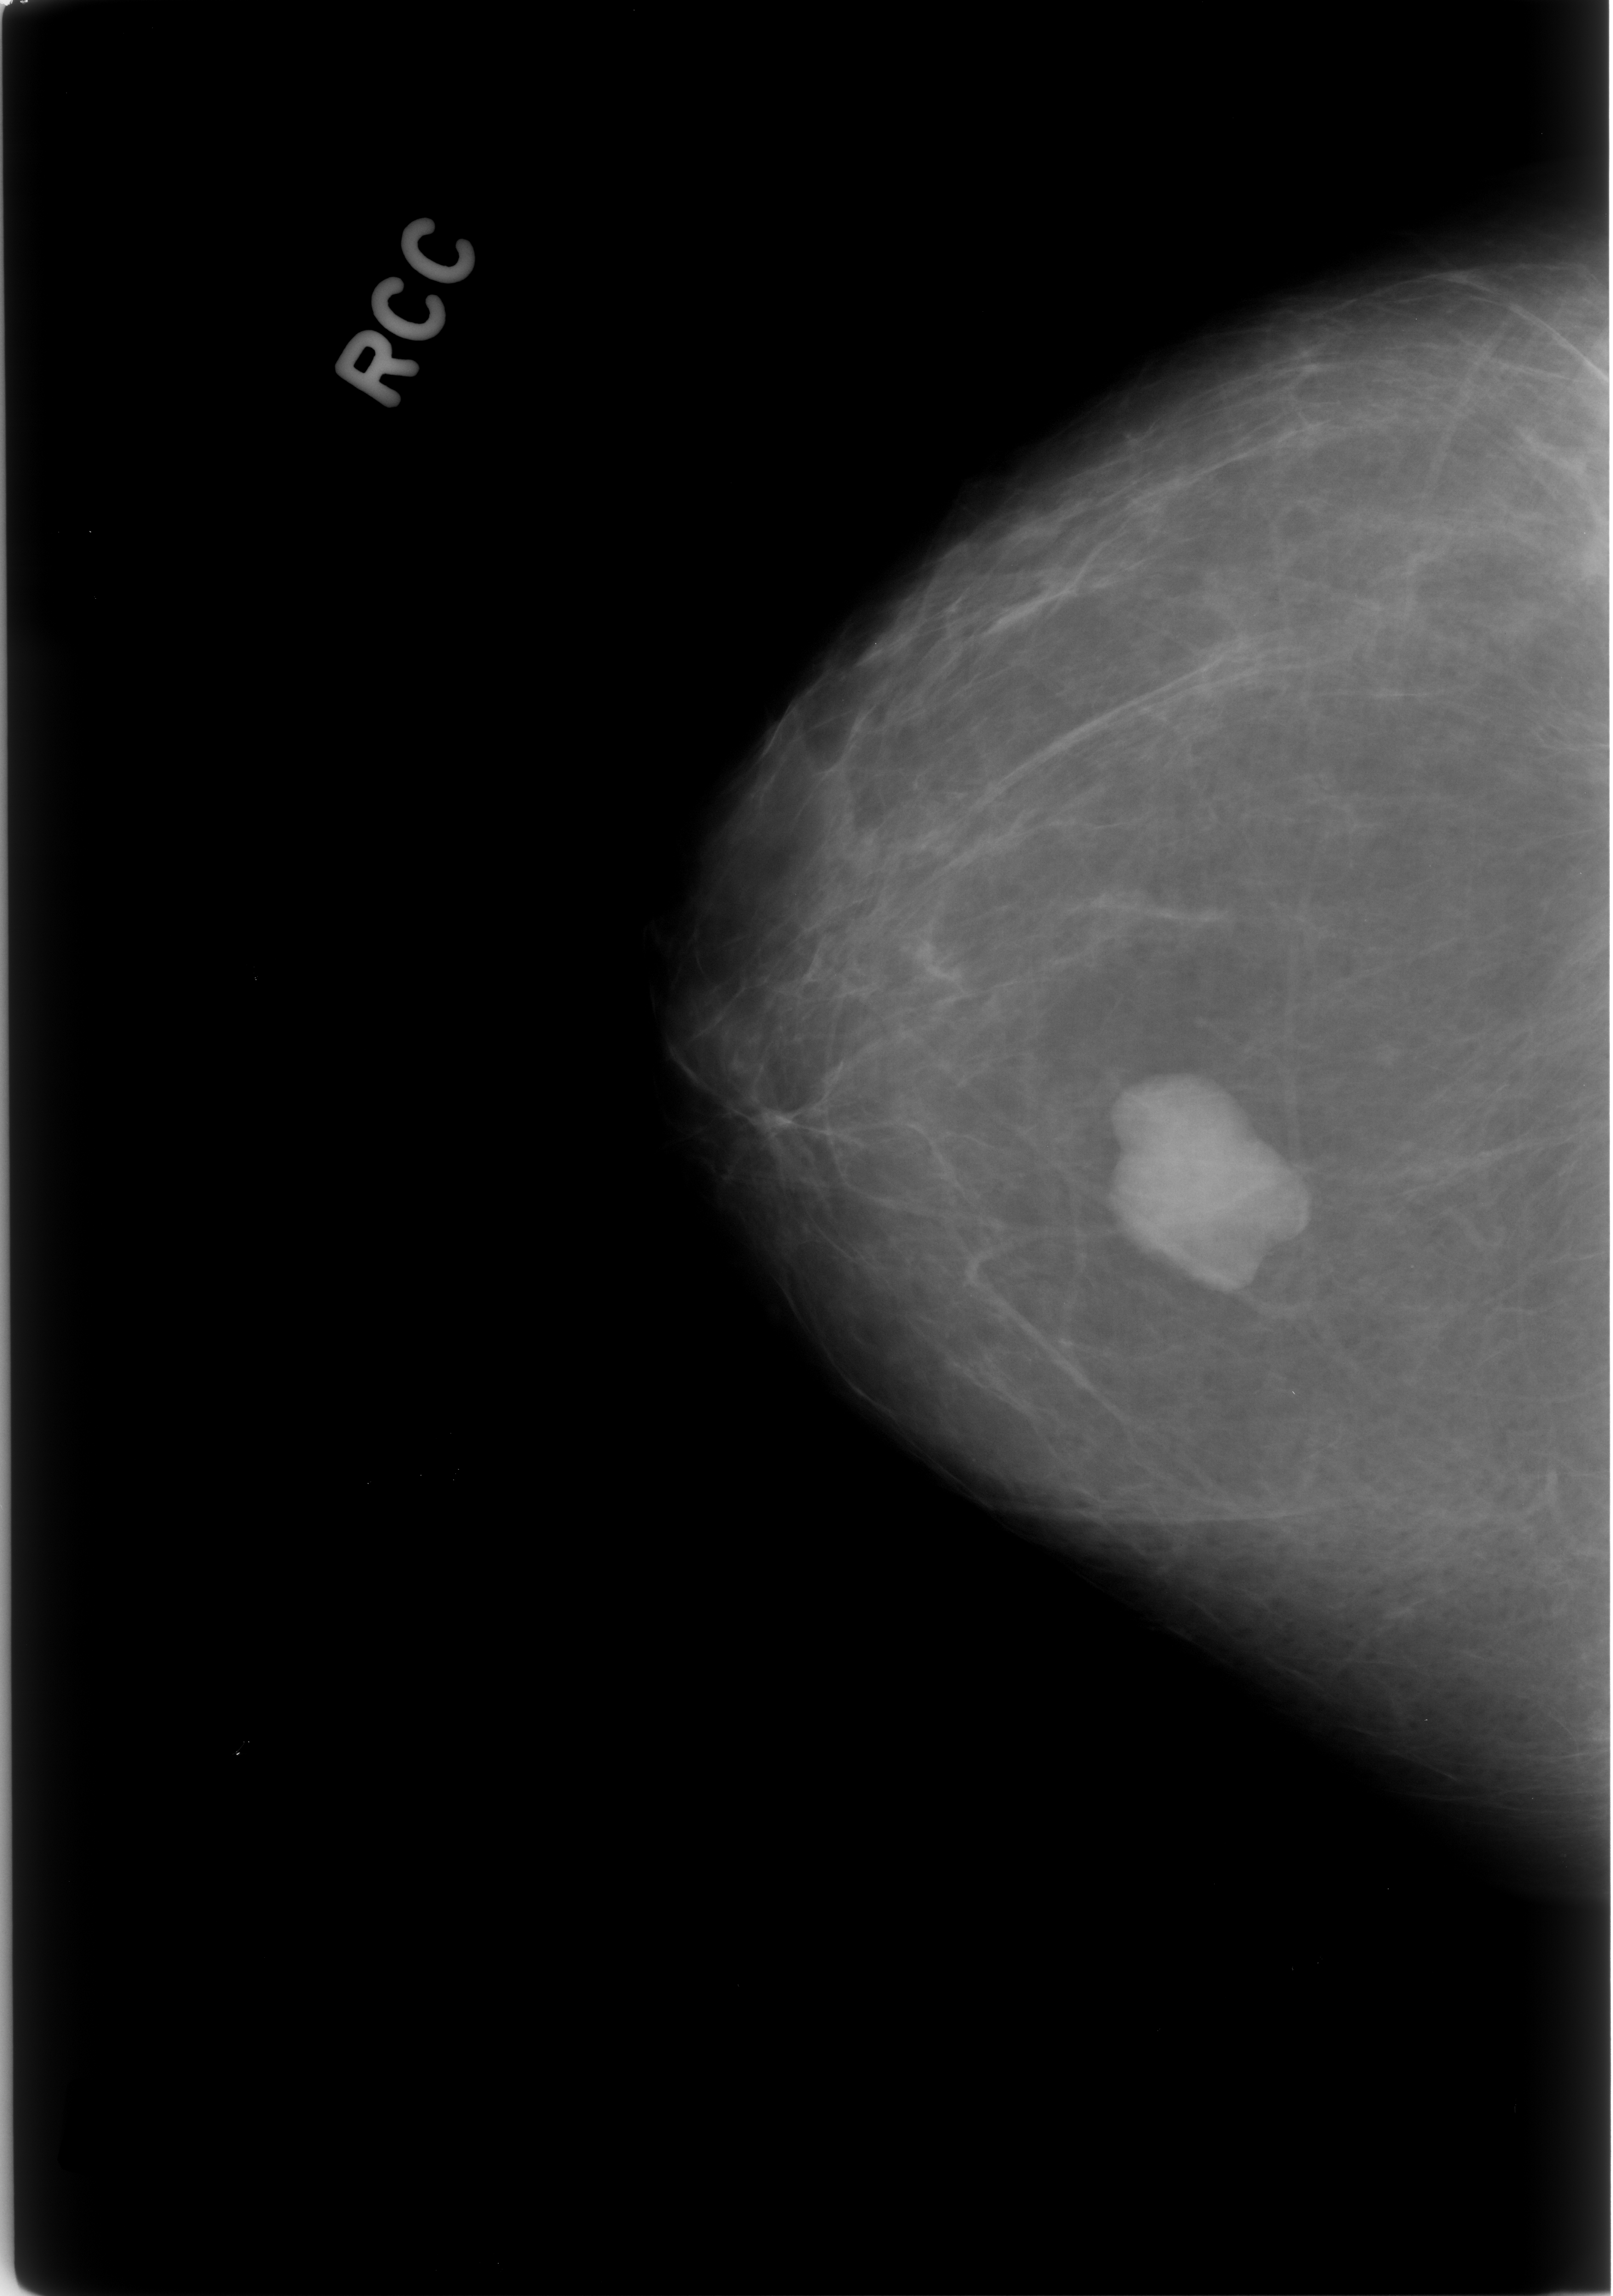
Scanned film-screen mammogram; right breast; craniocaudal (CC) view; breast composition: almost entirely fatty (BI-RADS density category 1 of 4).
- Radiologist-marked abnormalities on this image: mass, shape lobulated, margins circumscribed; BI-RADS assessment category 4; subtlety rating 5 on a 1 (subtle) to 5 (obvious) scale; pathology (as recorded): benign.